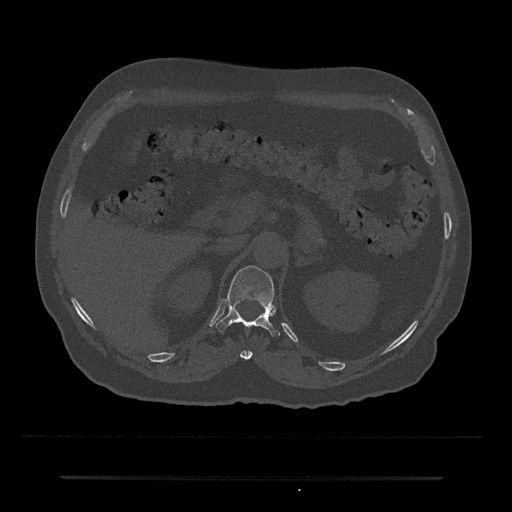
CT including the spine, one axial slice; slice 134 of 797 in the series (ordered by position); 120 kVp; bone window (W 1800 / L 400 HU); 0.5 mm slice thickness; 512 × 512 image matrix, field of view 437 × 437 mm. Patient: male, 69 years. From the clinical record (not read from this slice): primary cancer: prostate.
Annotated regions visible in this slice (semi-automatic segmentation, software-assisted and operator-edited):
- T11 vertebra: bounding box [x1, y1, x2, y2] px = [240, 350, 252, 360]
- T12 vertebra: [215, 266, 280, 337]